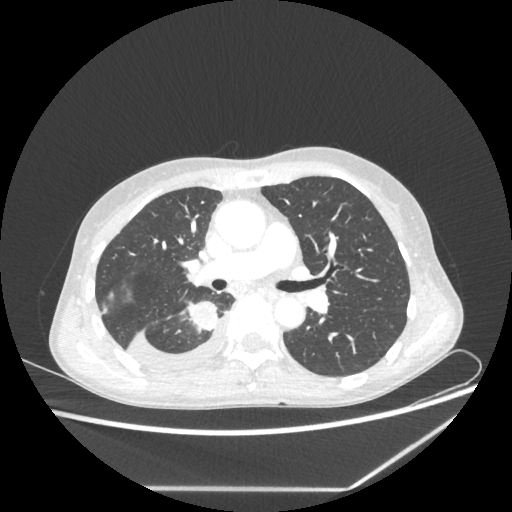
Chest CT, one axial slice; position 136 of 237 along the scan axis; 80 kVp; lung window (W 1500 / L -600 HU); 1.25 mm slice thickness; 512 × 512 image matrix, field of view 364 × 364 mm. Patient: female, 59 years. From the clinical record (not read from this slice): clinical TNM (as recorded): T1c N1 M1.
Annotated regions visible in this slice (rectangle marked by the reading radiologist):
- lung tumour (recorded histology: adenocarcinoma): bounding box [x1, y1, x2, y2] px = [186, 298, 222, 336]